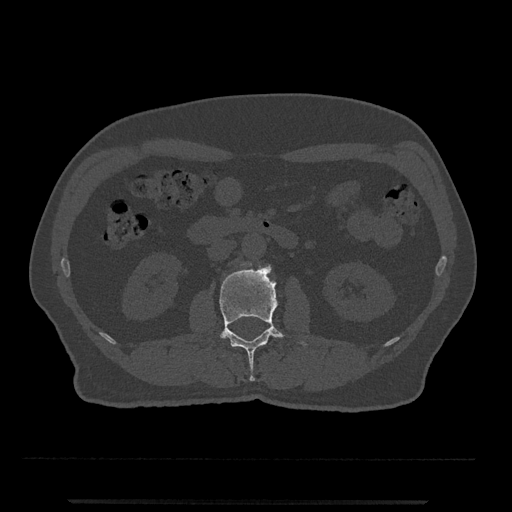
CT including the spine, one axial slice. Position 262 of 797 along the scan axis. Reconstruction kernel Br40s/3. Bone window (W 1800 / L 400 HU). 0.5 mm slice thickness. 512 × 512 image matrix, field of view 419 × 419 mm. Male patient, age 63 years. From the clinical record (not read from this slice): primary cancer: prostate.
Annotated regions visible in this slice (semi-automatic segmentation, software-assisted and operator-edited):
- L2 vertebra: box from (x=219, y=263) to (x=307, y=382) px